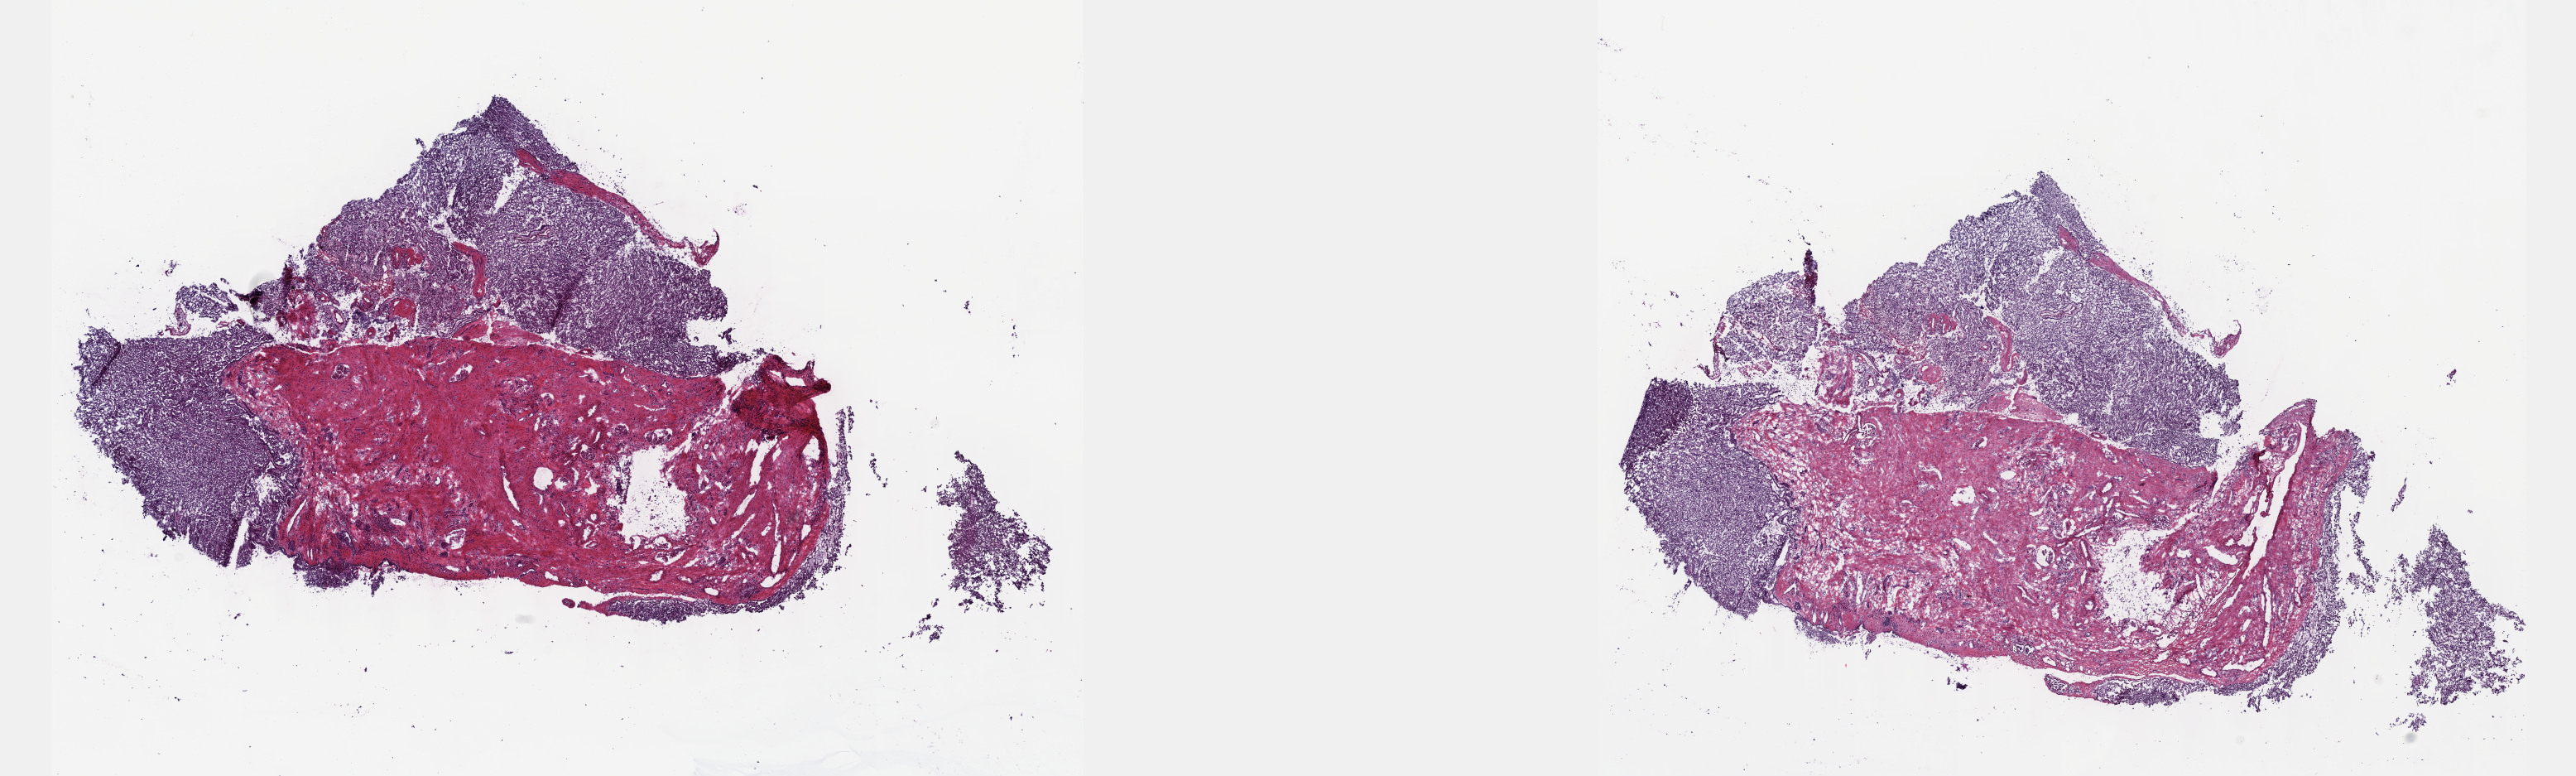
Whole-slide histology image, Hematoxylin and eosin (H&E) stained, low-resolution overview of the scanned area, about 25.1 x 7.6 mm (acquisition: 40x scan); frozen section; primary tumour sample from the kidney. Male, age 62 years at initial diagnosis. Composition of this section per pathologist review: tumour cells 40%, tumour nuclei 70%, normal cells 5%, stromal cells 55%, necrosis 0%. Inflammatory infiltration, as recorded: lymphocyte infiltration 10%, monocyte infiltration 2%, neutrophil infiltration 2%.
Pathologic diagnosis: Papillary adenocarcinoma, NOS. Laterality: left. AJCC pathologic stage: I (6th edition).